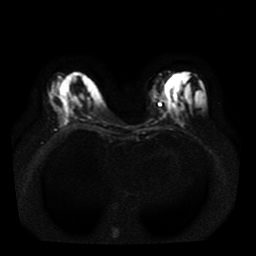
Breast MRI, one axial slice. Position 13 of 41 along the scan axis. Diffusion-weighted series; image 2 of 4 stored at this slice position (different b-values; order by instance number). 1.5 T. 5 mm slice thickness. 256 × 256 image matrix, field of view 330 × 330 mm. Female patient.
Annotated regions visible in this slice (expert manual segmentation):
- tumour on diffusion-weighted imaging: bounding box <67,92,72,95> (left, top, right, bottom; pixels)